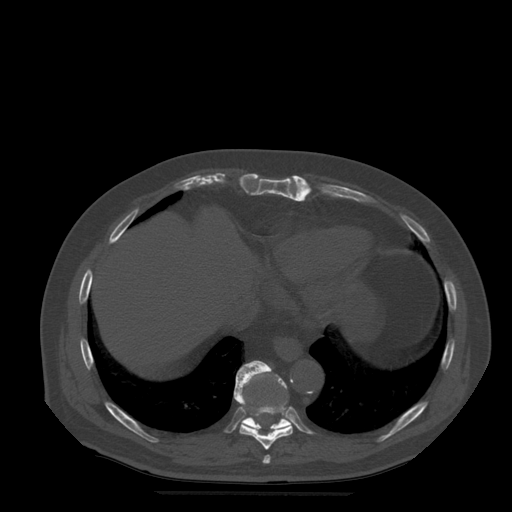
CT including the spine, one axial slice. Slice 282 of 522 in the series (ordered by position). Bone window (W 1800 / L 400 HU). 1.25 mm slice thickness. 512 × 512 image matrix. Patient age 72 years. Case-level facts recorded for this patient, not image findings: primary cancer: prostate.
Annotated regions visible in this slice (semi-automatic segmentation, software-assisted and operator-edited):
- T10 vertebra: bounding box [x1, y1, x2, y2] px = [236, 361, 291, 432]
- T8 vertebra: [263, 455, 271, 464]
- T9 vertebra: [234, 366, 293, 450]